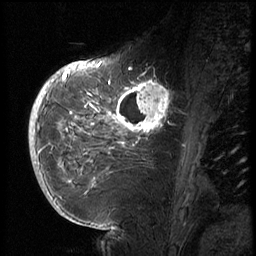
Breast MRI (dynamic contrast-enhanced), one sagittal slice; position 24 of 72 along the scan axis; 3 images stored at this slice position (order not interpretable as contrast timing); 1.5 T; TE 4.2 ms, TR 8.9 ms; 256 × 256 image matrix, field of view 200 × 200 mm. Female patient, age 56 years. From the clinical record (not read from this slice): setting: breast cancer imaged before/during neoadjuvant chemotherapy.
Structures marked on this image (semi-automatically segmented with operator editing):
- analysis volume of interest (the breast-tissue region the enhancement analysis was run in; not a lesion): box from (x=114, y=76) to (x=177, y=138) px
- tumour enhancement mask (voxels above the 140 % enhancement threshold inside the analysis volume of interest): (x=116, y=79)–(x=172, y=133)